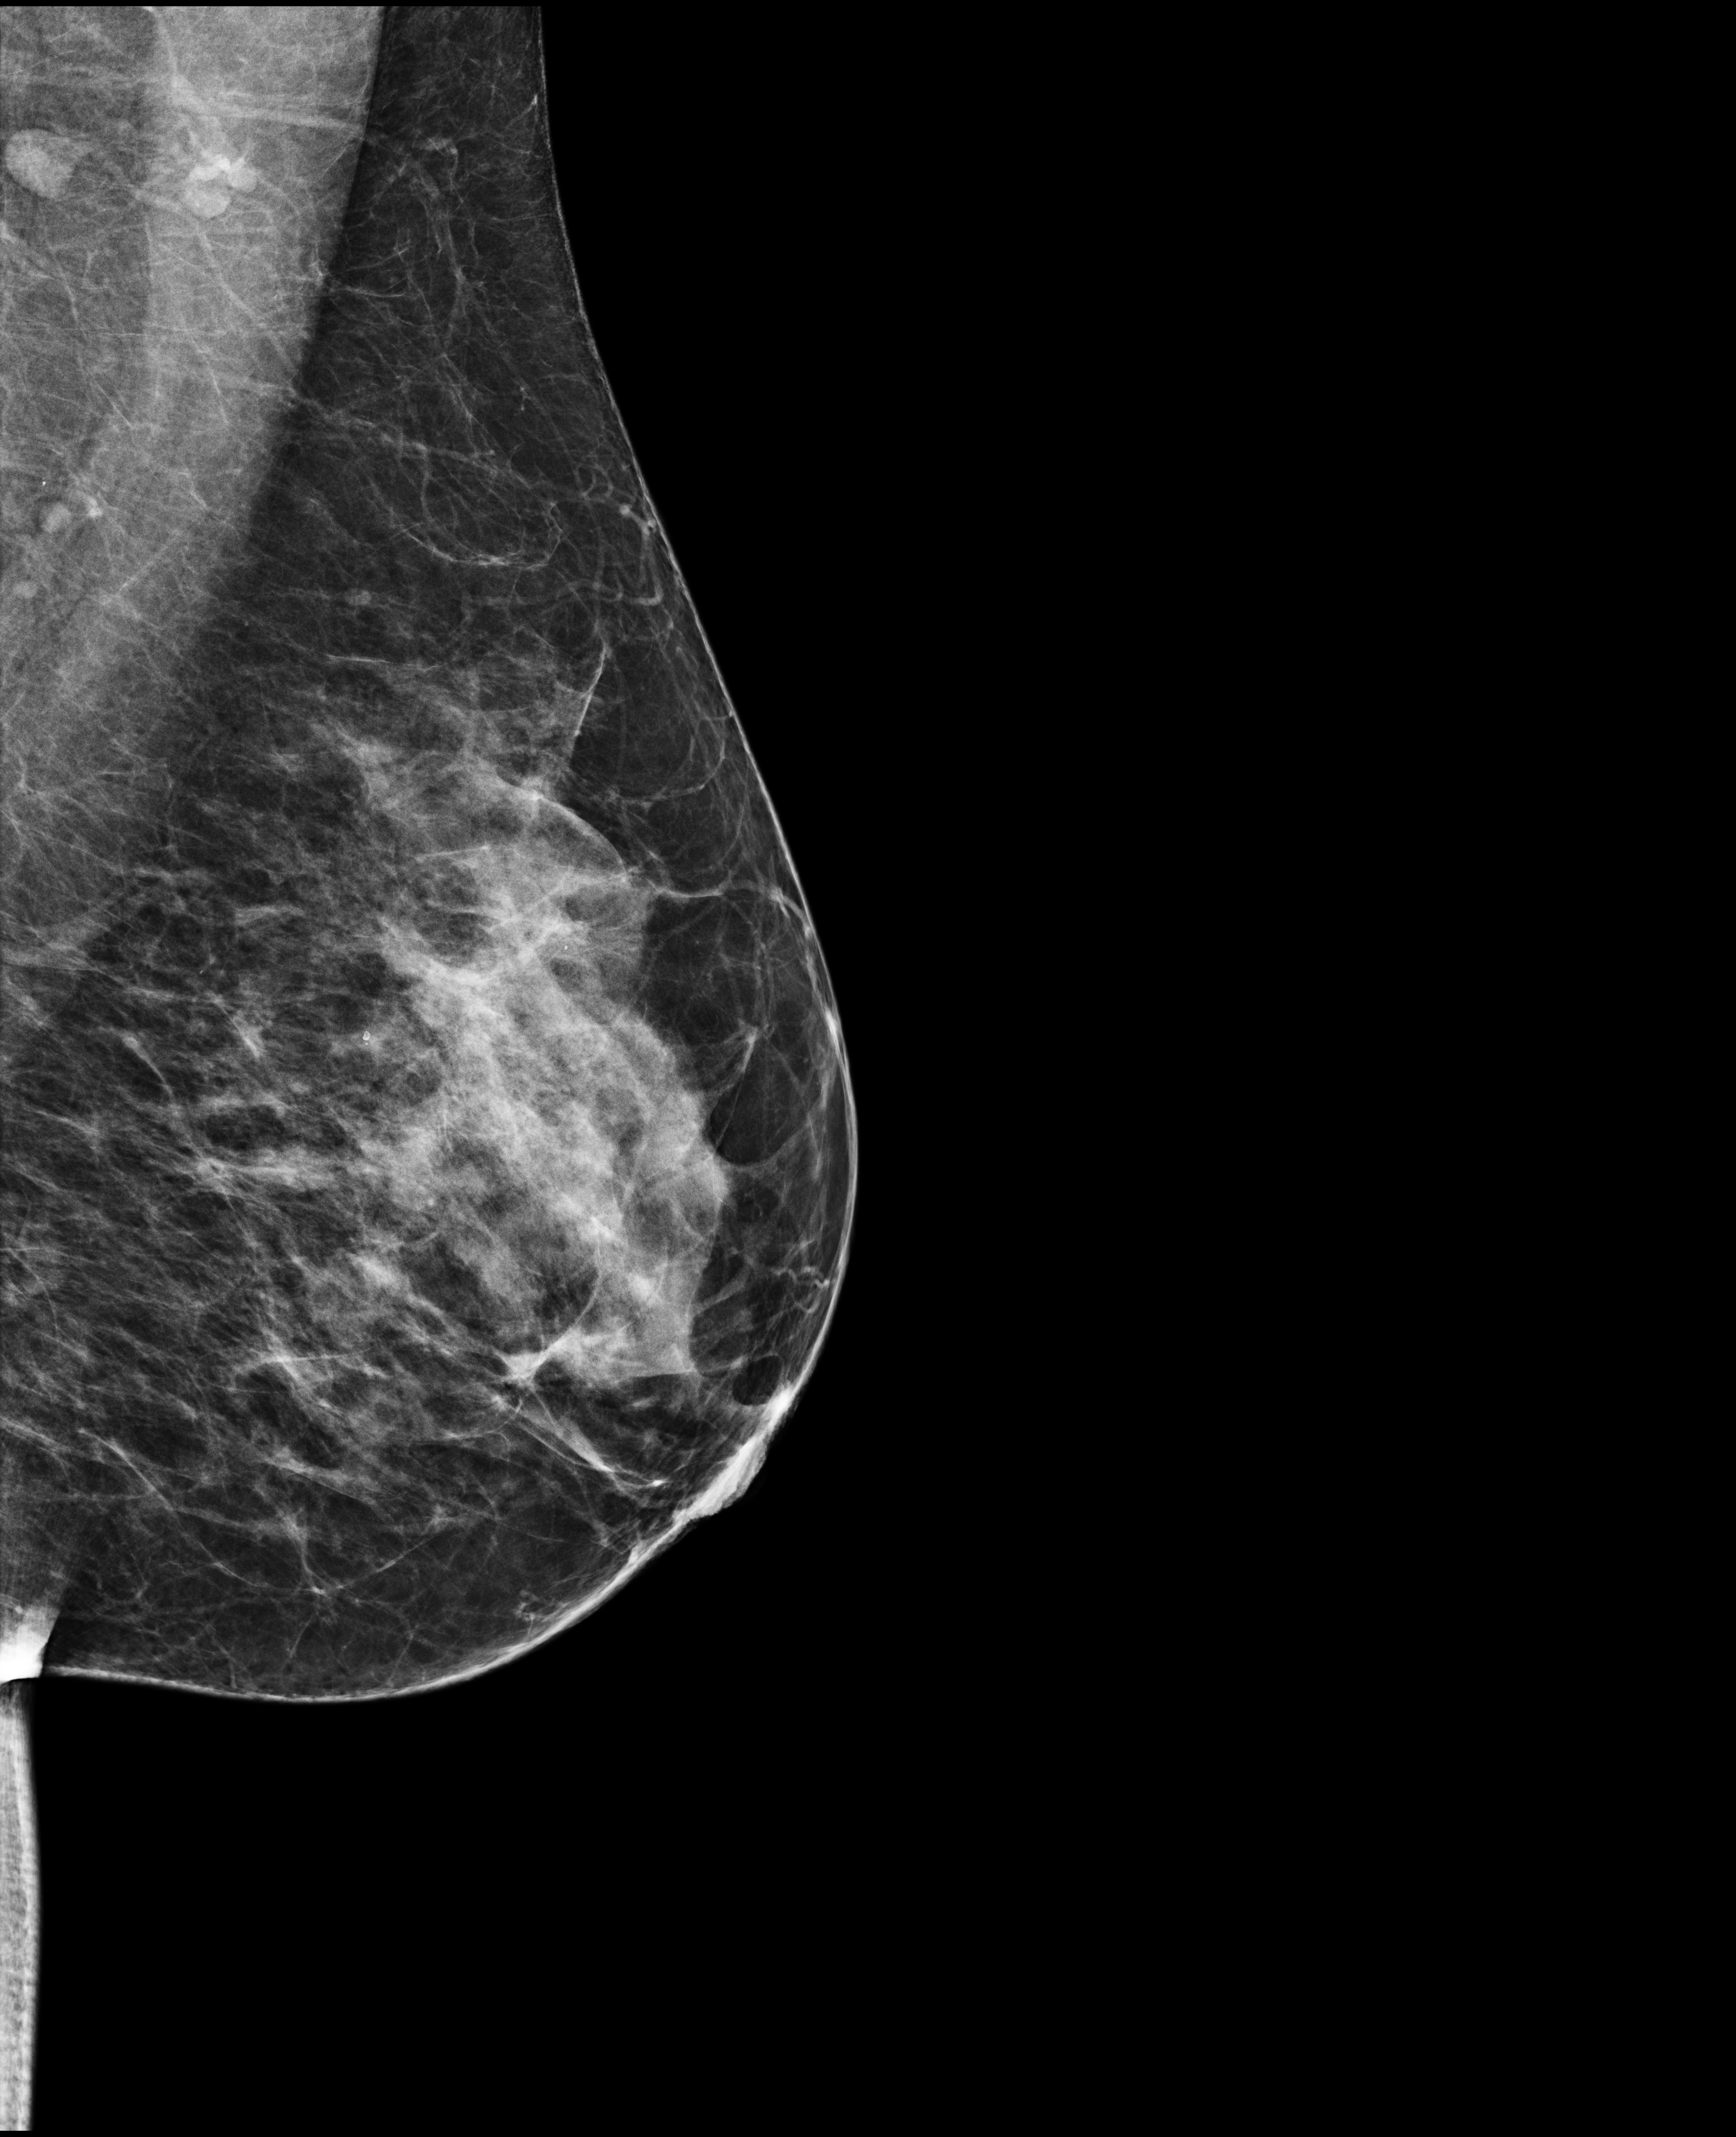
Full-field digital mammogram (FFDM), left breast, medio-lateral oblique projection, screening examination, system: Selenia Dimensions. Patient: female, 48 years.
Breast density at the screening exam (both breasts): heterogeneously dense (BI-RADS density category c). Final BI-RADS assessment for this screening round (tomosynthesis exam, both breasts): category 1. Recall: no recall after this screen.